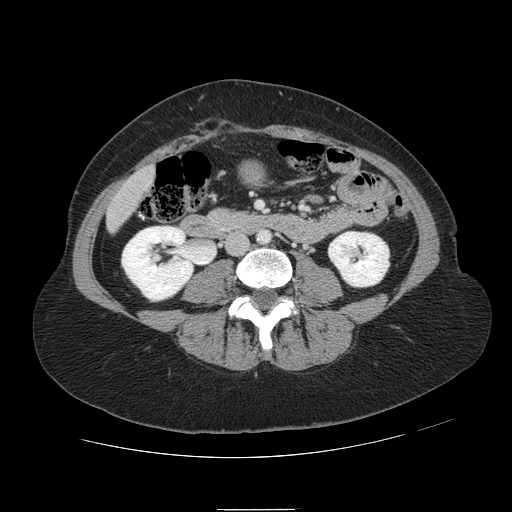
Contrast-enhanced abdominal CT, one axial slice; slice 7 of 121 in the series (ordered by position); intravenous contrast given; soft-tissue window (W 400 / L 40 HU); 2.5 mm slice thickness; 512 × 512 image matrix, field of view 400 × 400 mm. Female patient, age 52 years. From the clinical record (not read from this slice): diagnosis: colorectal cancer liver metastases, imaged before liver resection; multiple liver metastases: yes; largest metastasis: 6.3 cm.
Annotated regions visible in this slice (expert manual segmentation):
- liver: bounding box [x1, y1, x2, y2] px = [108, 168, 155, 230]